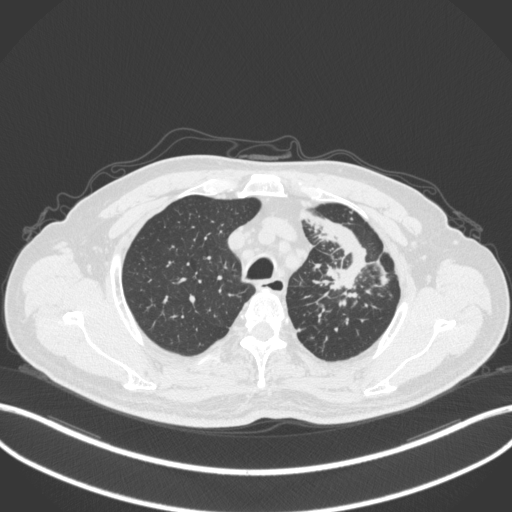
Chest CT, one axial slice. Slice 288 of 386 in the series (ordered by position). Reconstruction kernel B31f. 120 kVp. Lung window (W 1500 / L -600 HU). 512 × 512 image matrix. Patient: male, 69 years. From the clinical record (not read from this slice): clinical TNM (as recorded): T2a N2 M0; histopathological grade: G2-3.
Annotated regions visible in this slice (bounding box drawn by a radiologist):
- lung tumour (recorded histology: adenocarcinoma): box from (x=305, y=211) to (x=373, y=300) px